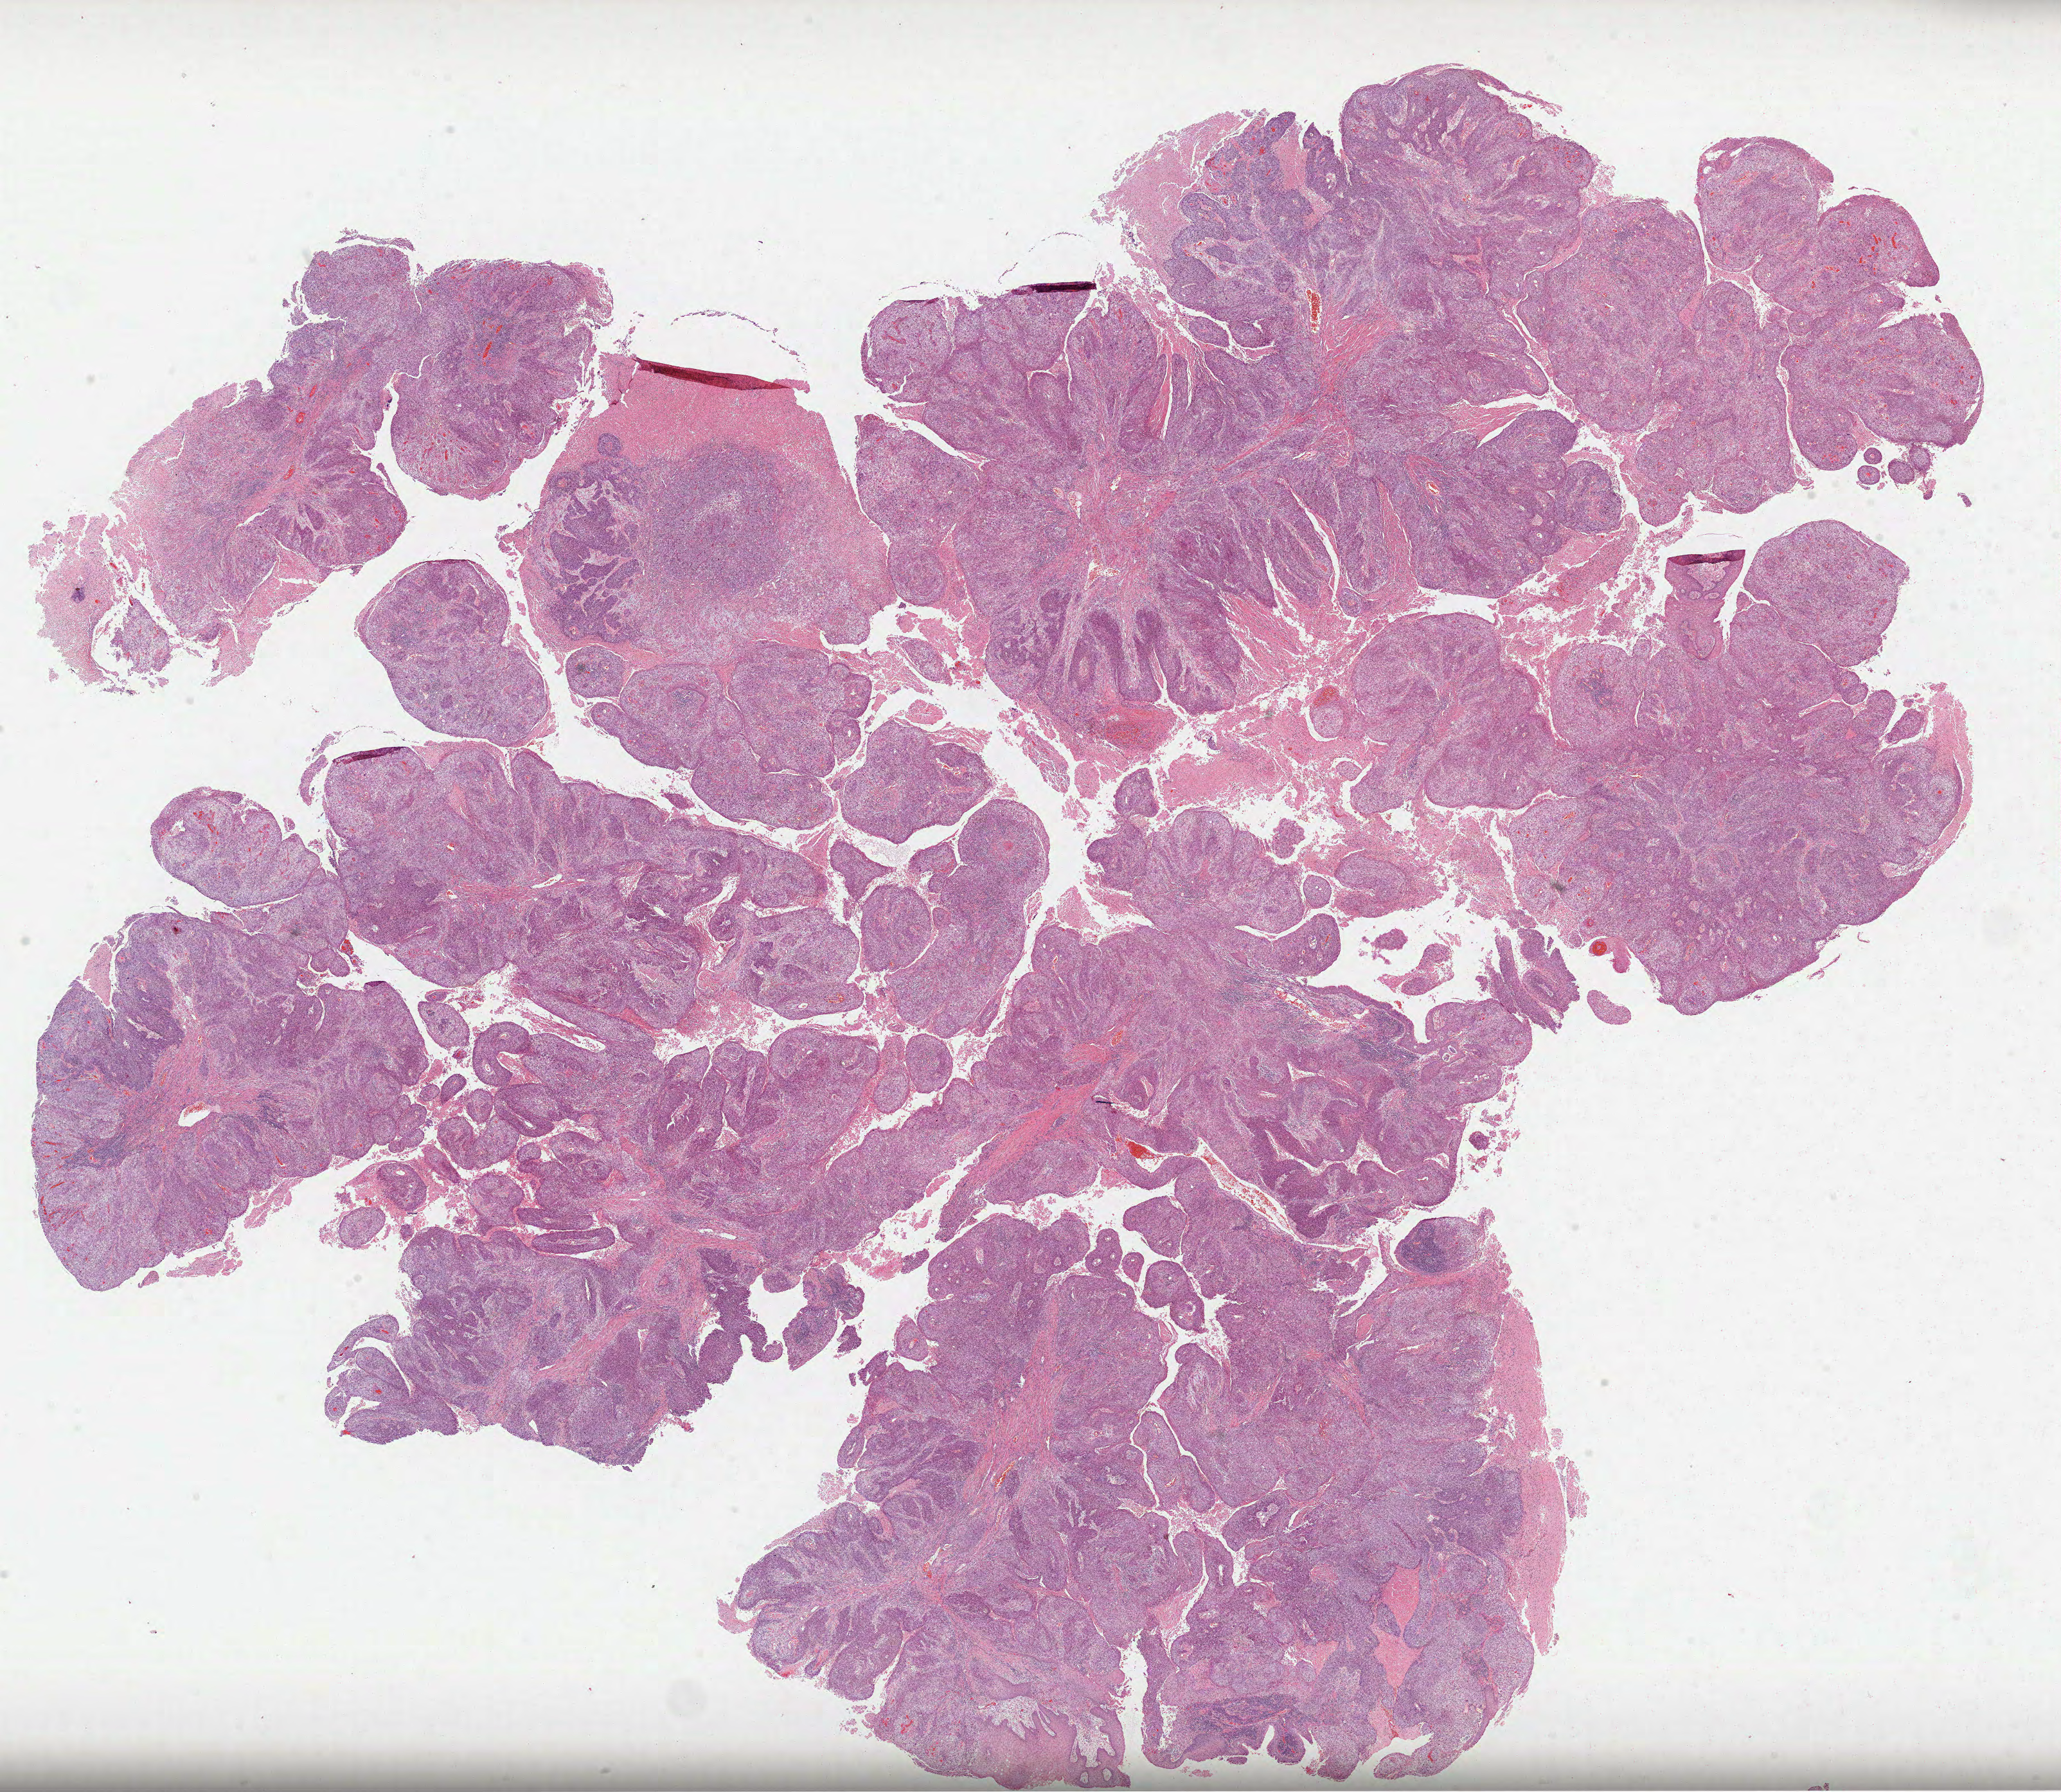
Whole-slide histology image, H&E-stained — shown as a low-resolution overview of the whole scanned area (about 25.9 x 22.5 mm); FFPE section; sample: primary tumour, head and neck. Male patient; age at initial diagnosis 65 years. Histologic grade: G3 (poorly differentiated).
• laterality: right
• diagnosis: Squamous cell carcinoma, NOS